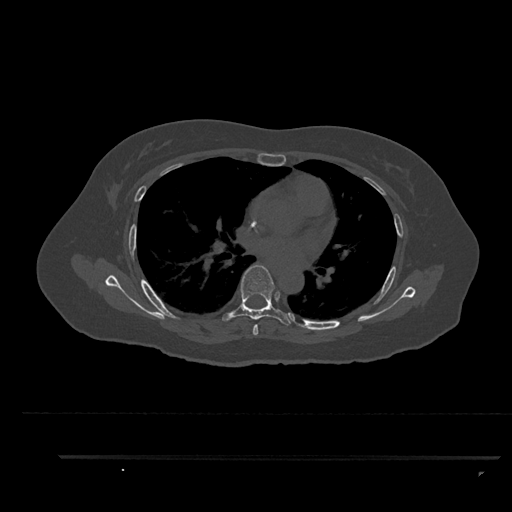
CT including the spine, one axial slice. Reconstruction kernel Br40s/3. Bone window (W 1800 / L 400 HU). 0.5 mm slice thickness. 512 × 512 image matrix, field of view 408 × 408 mm. Female patient, age 44 years. From the clinical record (not read from this slice): primary cancer: renal.
Outlined on this slice (semi-automatic segmentation, software-assisted and operator-edited):
- T5 vertebra: bounding box <253,324,258,335> (left, top, right, bottom; pixels)
- T6 vertebra: <222,264,295,326>